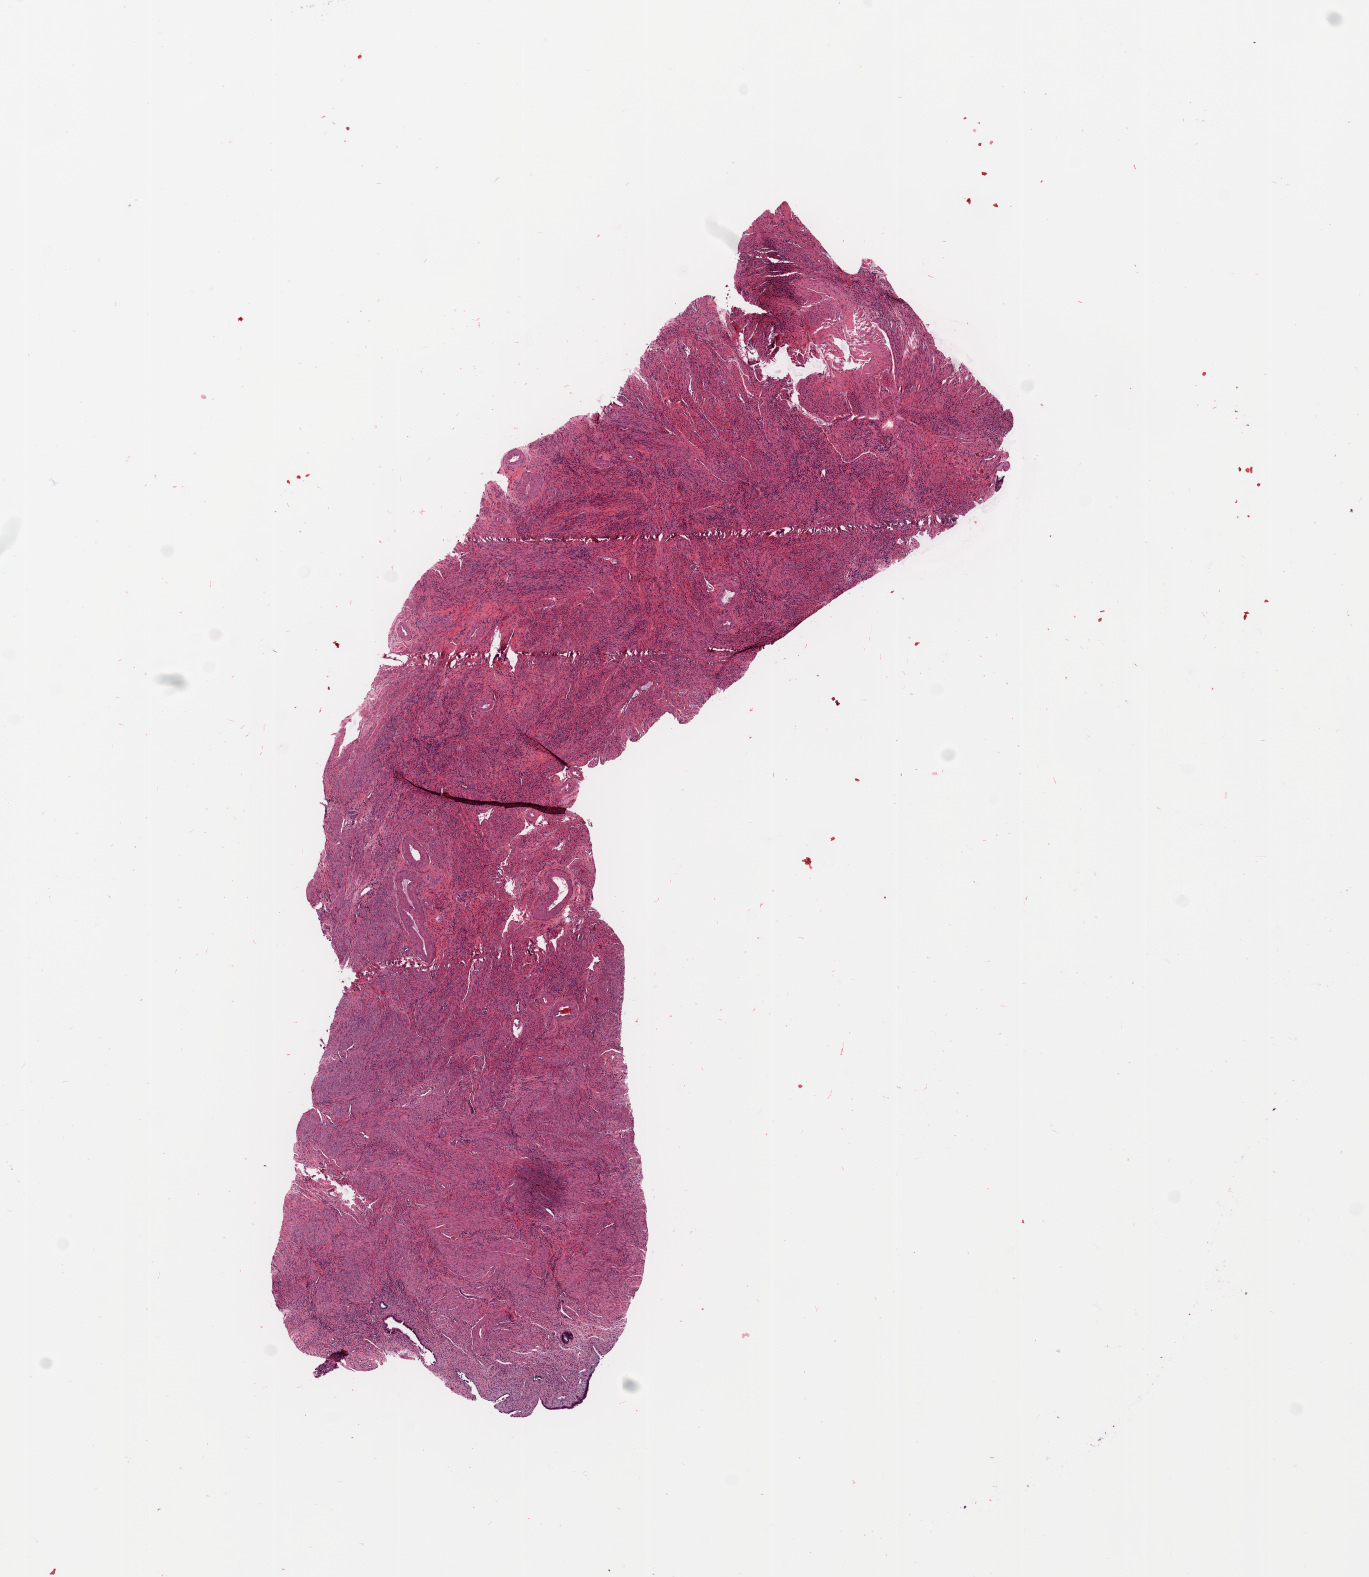
Hematoxylin and eosin (H&E) stained whole-slide image — whole scanned area (about 10.8 x 12.5 mm) shown as a low-resolution overview; normal (non-tumour) tissue sample, uterus. 63-year-old female patient.
* this section: normal (non-tumour) tissue from the same patient
* patient diagnosis: Endometrioid adenocarcinoma, NOS